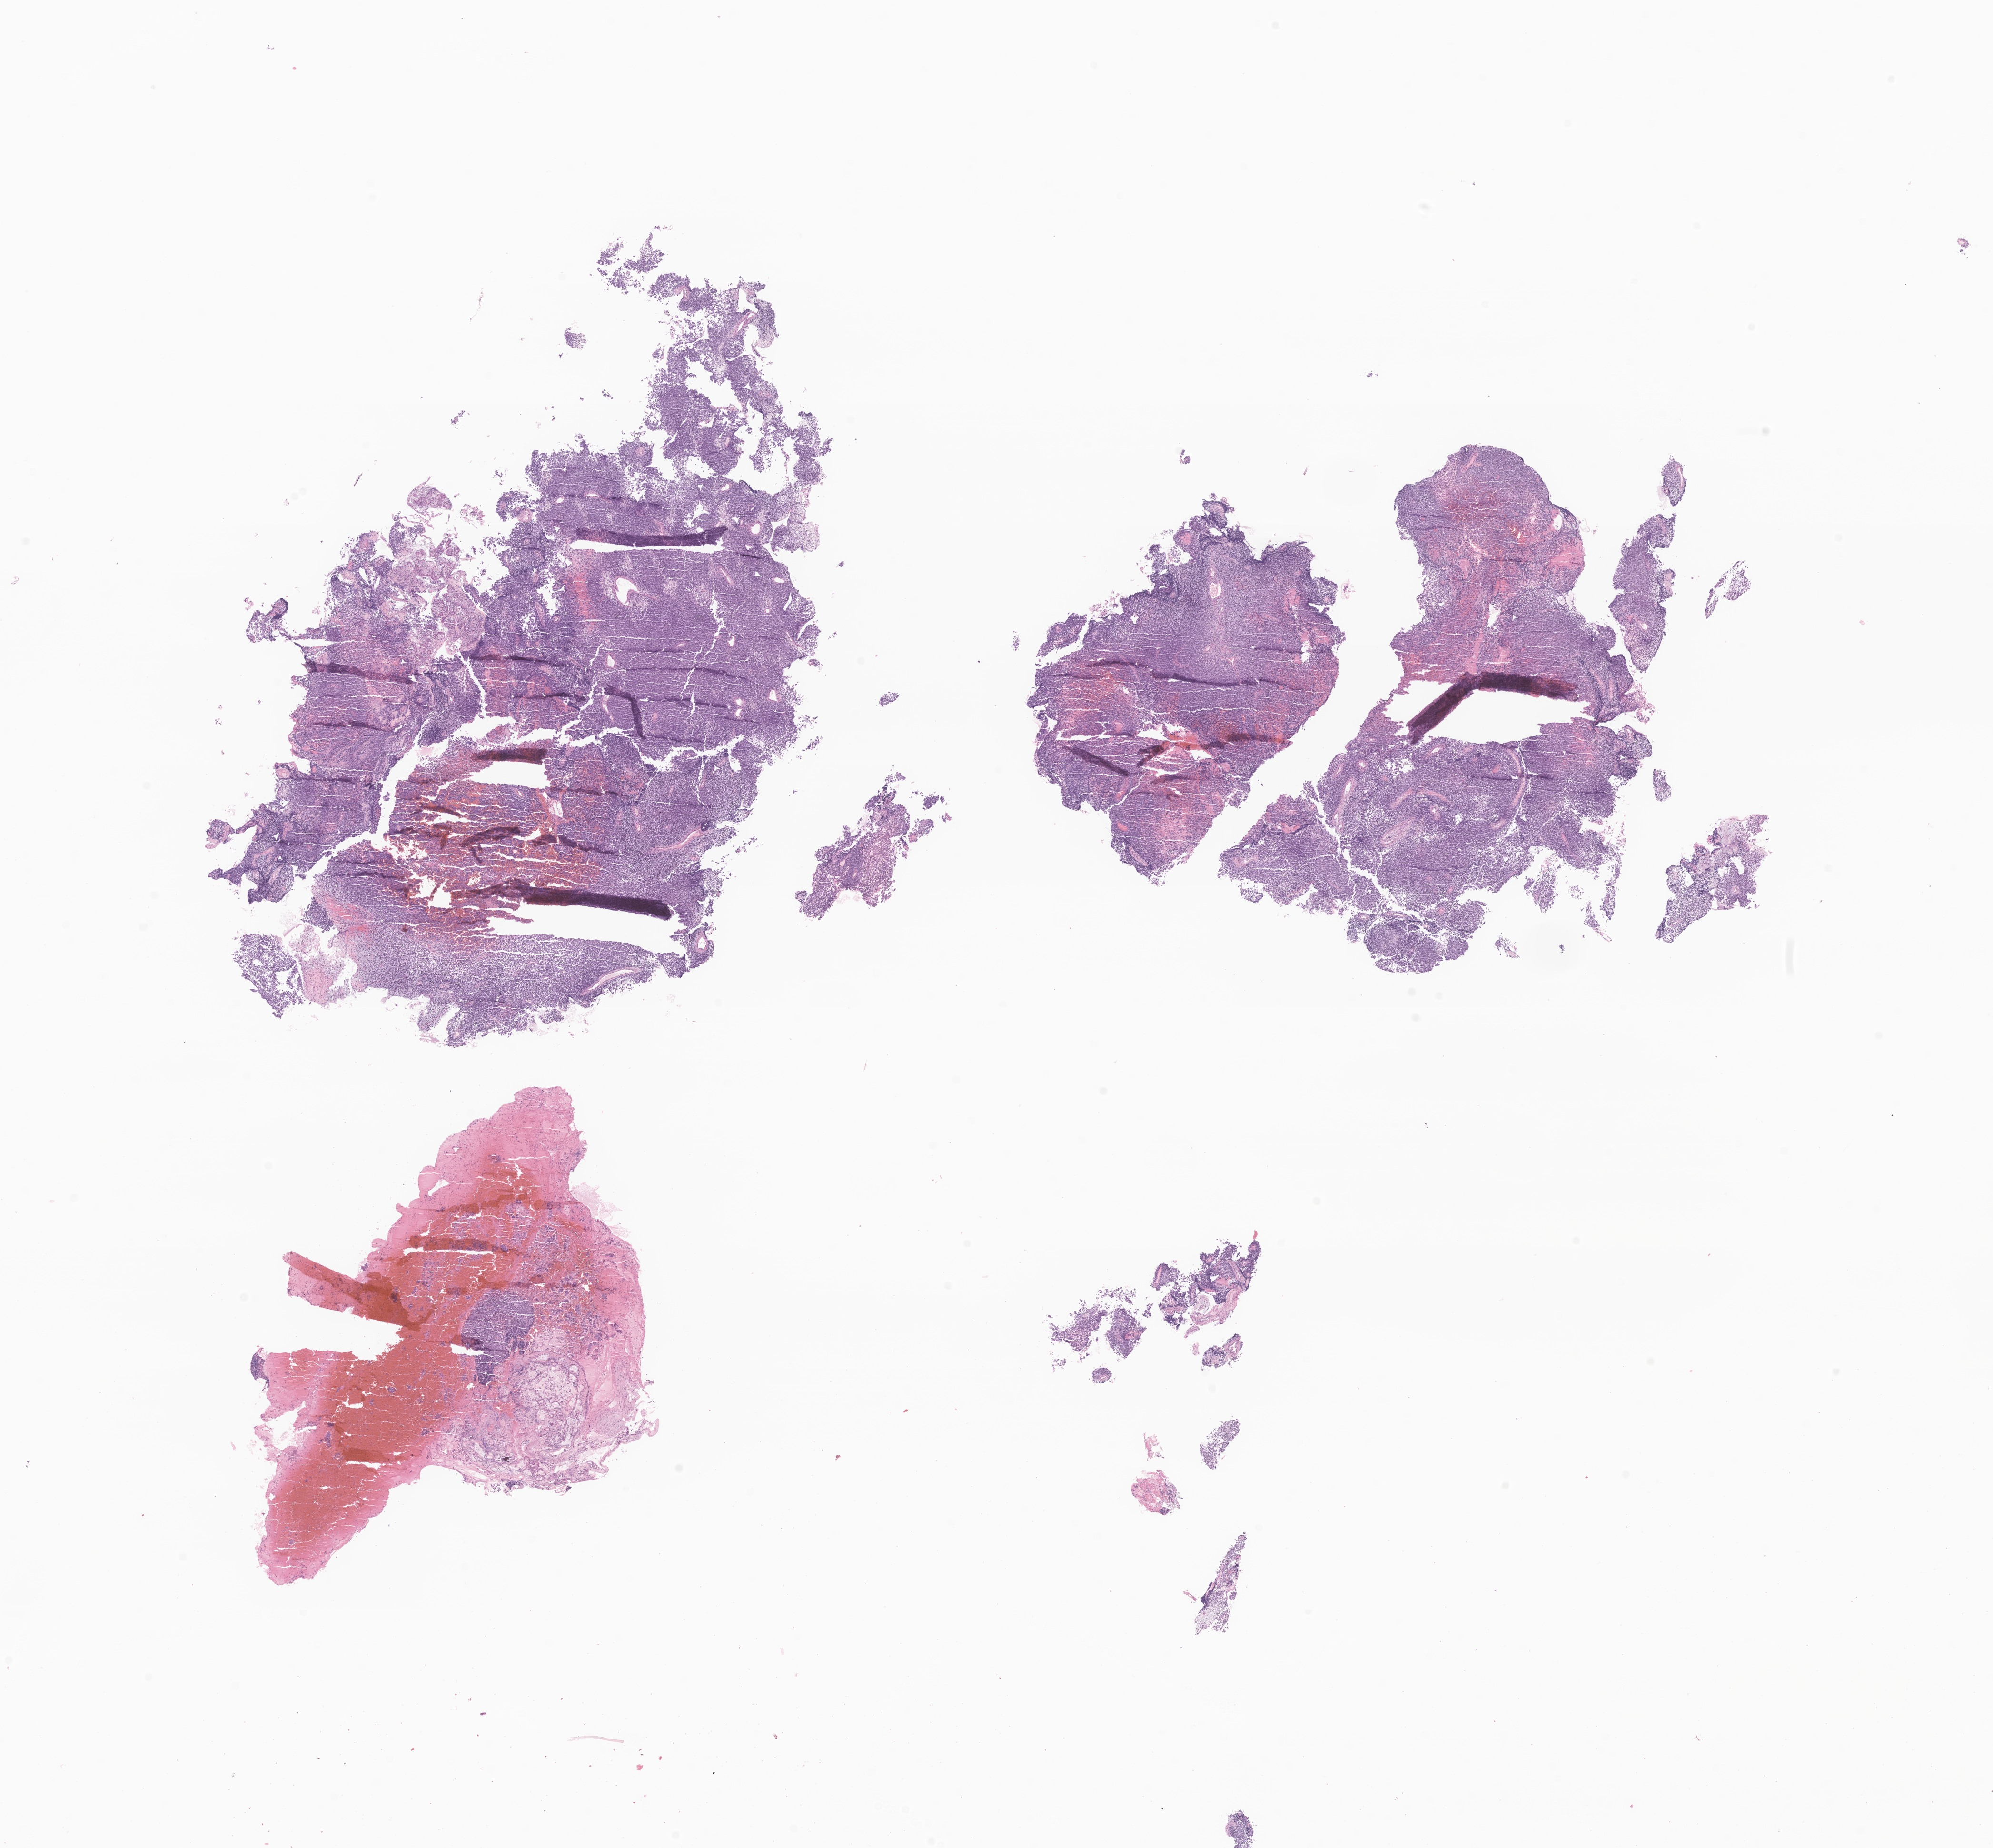
Whole-slide image, hematoxylin and eosin (H&E) stain of tumor tissue from the maxillary sinus — whole scanned area (about 17.7 x 16.4 mm) shown as a low-resolution overview. Formalin-fixed, paraffin-embedded (FFPE) tissue. Female patient, age 216 months (18 years).
* diagnosis (ICD-O-3 morphology term): Alveolar rhabdomyosarcoma